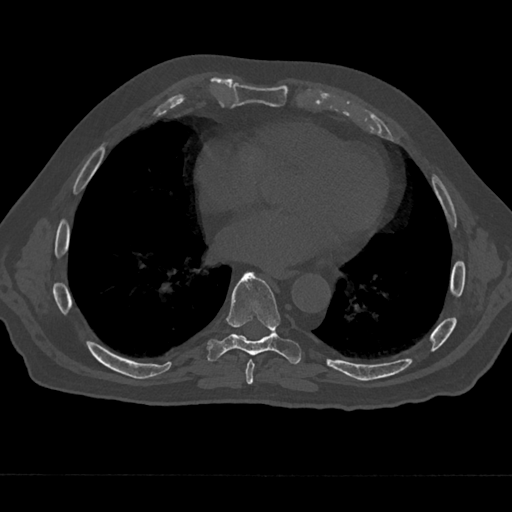
CT including the spine, one axial slice; slice 320 of 797 in the series (ordered by position); 120 kVp; bone window (W 1800 / L 400 HU); 0.5 mm slice thickness; 512 × 512 image matrix, field of view 377 × 377 mm. Male patient, age 75 years. Case-level facts recorded for this patient, not image findings: primary cancer: renal.
Outlined on this slice (semi-automatic segmentation, software-assisted and operator-edited):
- T7 vertebra: bounding box <243,359,259,385> (left, top, right, bottom; pixels)
- T8 vertebra: <206,272,301,365>